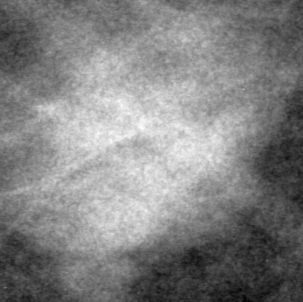
Region of interest cut from a scanned film mammogram (one marked finding); left breast; CC view; BI-RADS breast density category 3 (scale 1–4).
Marked abnormality: mass, shape lobulated, margins obscured; BI-RADS assessment category 4; pathology (as recorded): benign.